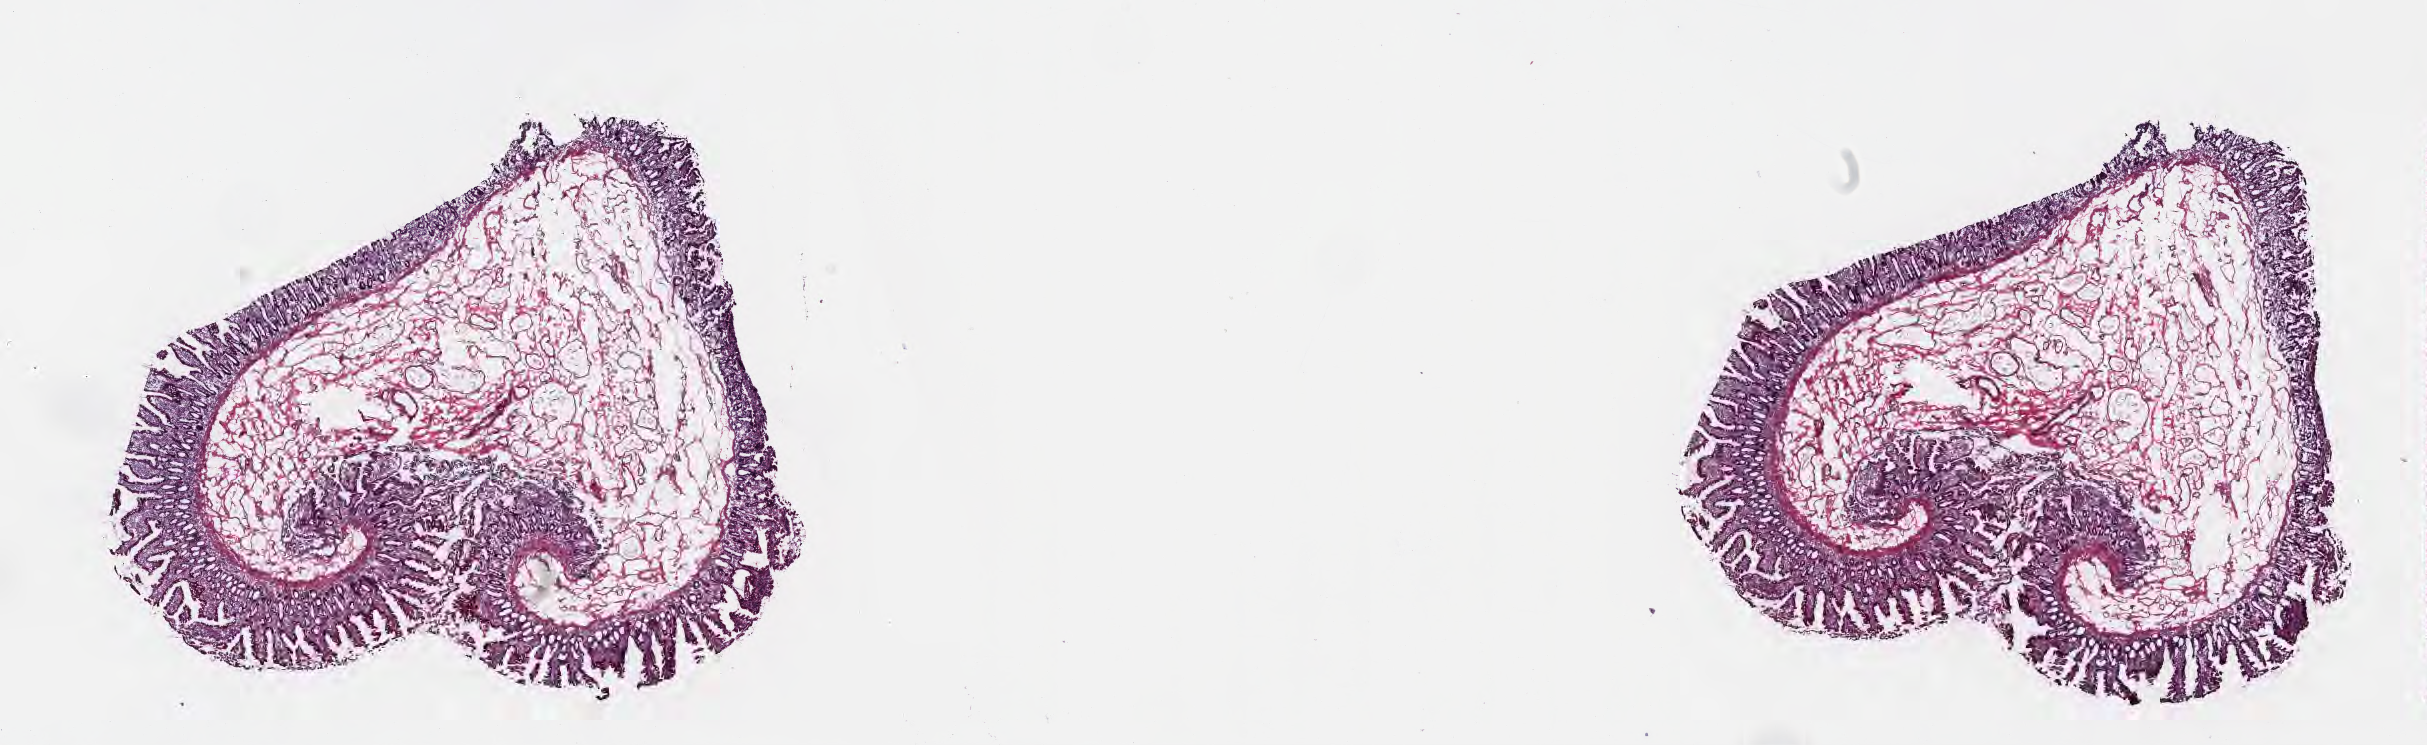
Haematoxylin and eosin whole-slide image — shown as a low-resolution overview of the whole scanned area (about 19.6 x 6.0 mm); frozen section (tissue freezing medium); specimen: non-tumor (normal tissue) sample from a patient with infiltrating duct carcinoma, NOS; site: head of pancreas. Patient: male, age at initial diagnosis 75 years. Slide review estimates, as recorded: tumor cells 0%, tumor nuclei 0%, stromal cells 47%, necrosis 0%, normal cells 53%. Infiltration values recorded for this section: lymphocyte infiltration 48%, monocyte infiltration 2%, neutrophil infiltration 0%.
This section: non-tumor tissue sample; the patient's diagnosis is given above. Section: bottom of the tissue portion.